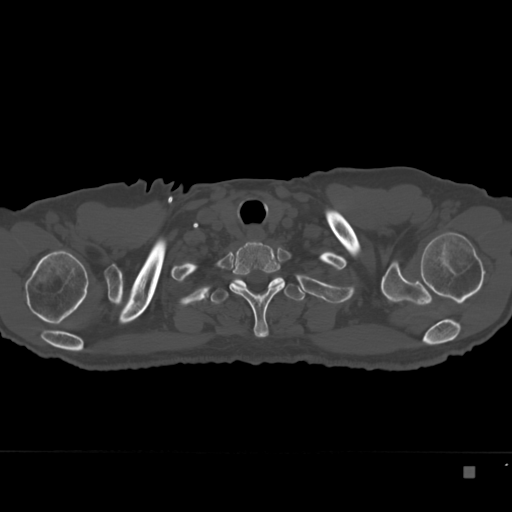
CT including the spine, one axial slice. Position 311 of 332 along the scan axis. Bone window (W 1800 / L 400 HU). 1.5 mm slice thickness. 512 × 512 image matrix, field of view 389 × 389 mm. Male patient, age 72 years. Case-level facts recorded for this patient, not image findings: primary cancer: skeletal.
Structures marked on this image (semi-automatic segmentation, software-assisted and operator-edited):
- T1 vertebra: bounding box [x1, y1, x2, y2] px = [230, 242, 283, 338]
- T2 vertebra: [211, 272, 306, 304]